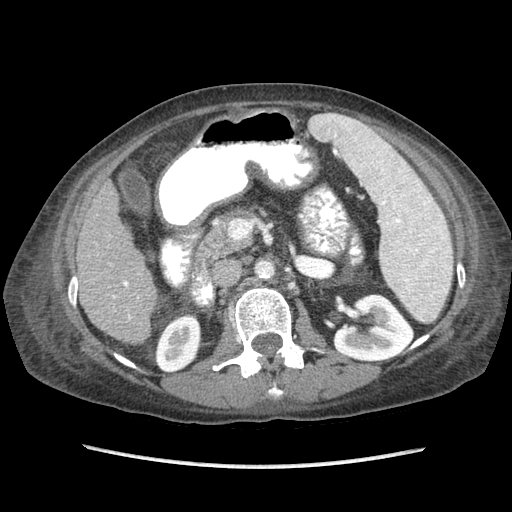
Contrast-enhanced abdominal CT (liver protocol), one axial slice. Position 31 of 87 along the scan axis. 120 kVp. Soft-tissue window (W 400 / L 40 HU). 2.5 mm slice thickness. 512 × 512 image matrix. From the clinical record (not read from this slice): diagnosis: hepatocellular carcinoma (patient treated with transarterial chemoembolisation; whether this scan precedes or follows treatment is not stated here); TNM stage (as recorded): Stage-IIIB.
Annotated regions visible in this slice (semi-automatically segmented with operator editing):
- liver parenchyma outside the tumour (the mass and vessels are separate outlines, so this box may not span the whole liver): box from (x=74, y=182) to (x=156, y=344) px
- liver vessels: (x=73, y=277)–(x=132, y=319)